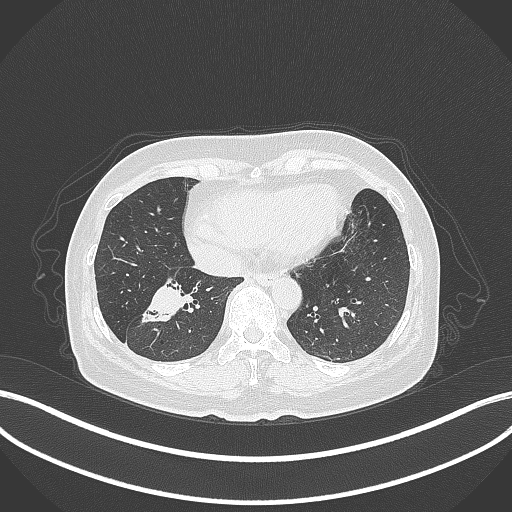
Chest CT, one axial slice. Slice 122 of 429 in the series (ordered by position). 120 kVp. Lung window (W 1500 / L -600 HU). 512 × 512 image matrix, field of view 400 × 400 mm. Patient: female, 67 years. Case-level facts recorded for this patient, not image findings: clinical TNM (as recorded): T1c N1 M0; histopathological grade: G2-3.
Outlined on this slice (rectangle marked by the reading radiologist):
- lung tumour (recorded histology: adenocarcinoma): bounding box (x1, y1, x2, y2) in pixels: (140, 276, 188, 326)